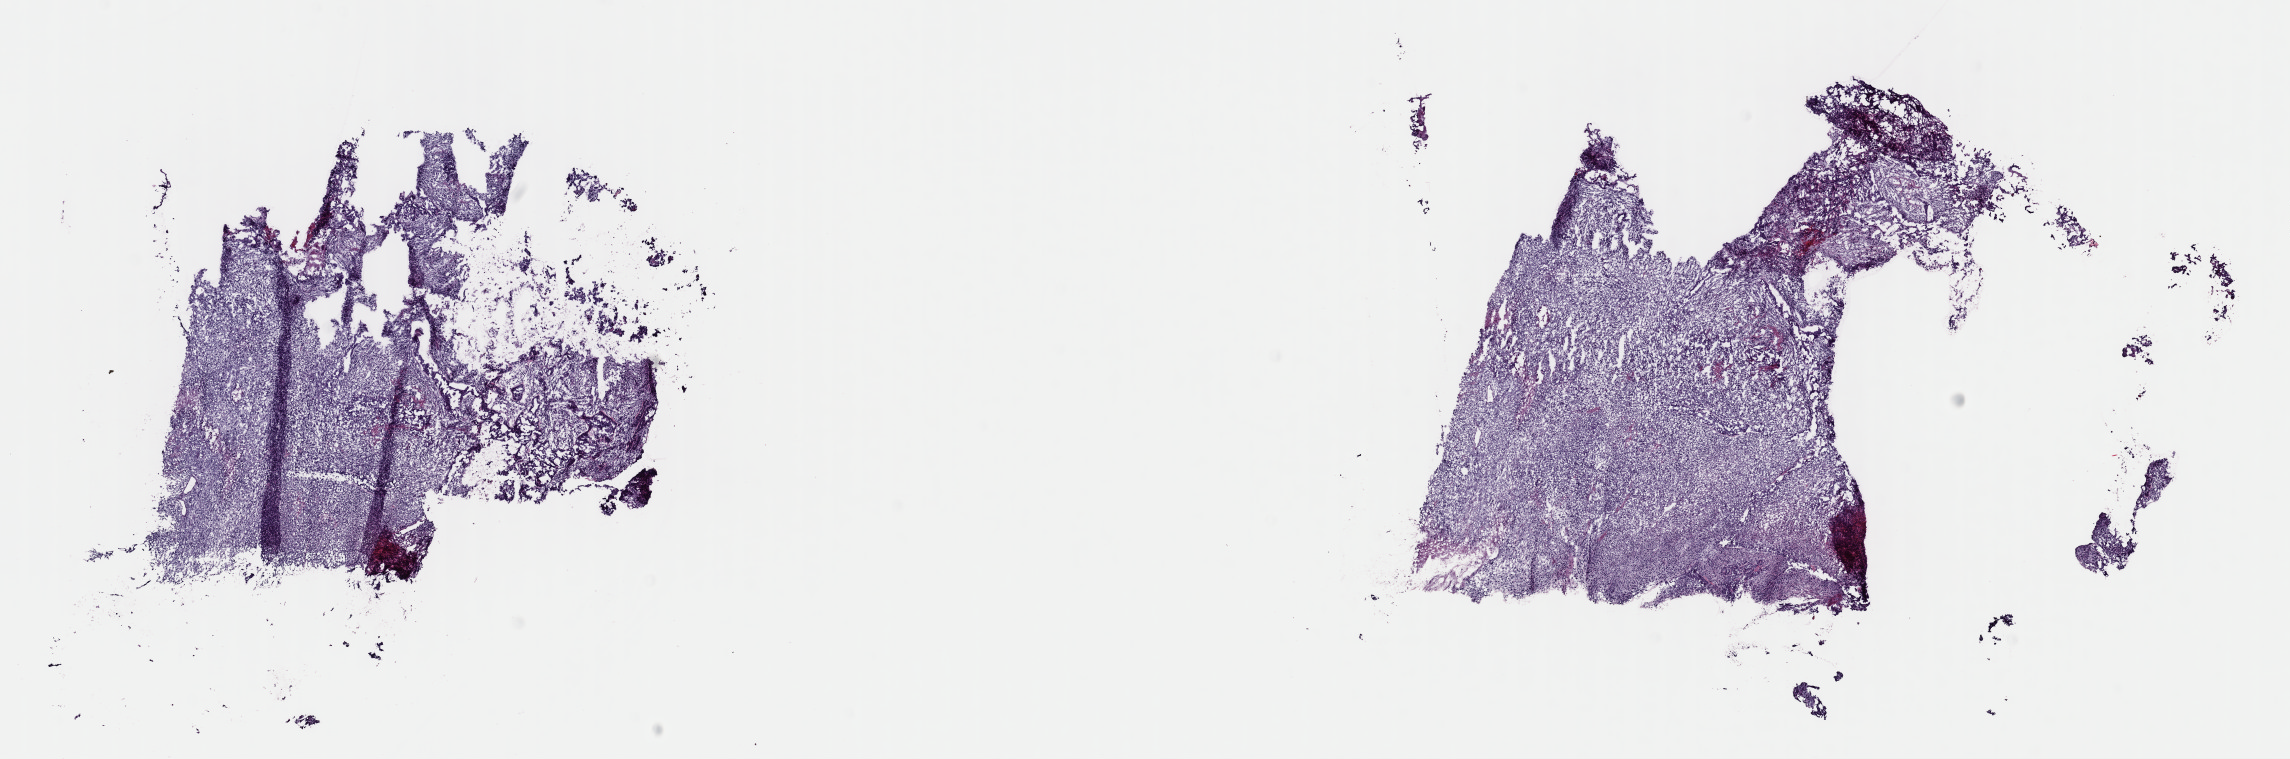
Digitized Hematoxylin and eosin (H&E) stained tissue section (whole slide), low-resolution overview of the scanned area, about 18.1 x 6.0 mm (acquisition: 40x scan); frozen section; uterus, primary tumour sample. Female patient; age at initial diagnosis 86 years. Histologic grade: G3 (poorly differentiated). Composition of this section per pathologist review: tumour cells 90%, tumour nuclei 95%, normal cells 0%, stromal cells 0%, necrosis 10%. Inflammatory infiltration, as recorded: lymphocyte infiltration 1%, monocyte infiltration 1%, neutrophil infiltration 0%.
Pathologic diagnosis: Serous cystadenocarcinoma, NOS. FIGO stage: IIIA.